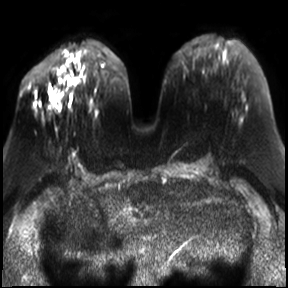
Breast MRI, one axial slice; slice 12 of 30 in the series (ordered by position); diffusion-weighted series; image 2 of 4 stored at this slice position (different b-values; order by instance number); 3 T; 288 × 288 image matrix, field of view 340 × 340 mm. Female patient.
Annotated regions visible in this slice (manually delineated by an expert):
- tumour on diffusion-weighted imaging: bounding box [x1, y1, x2, y2] px = [47, 72, 68, 104]